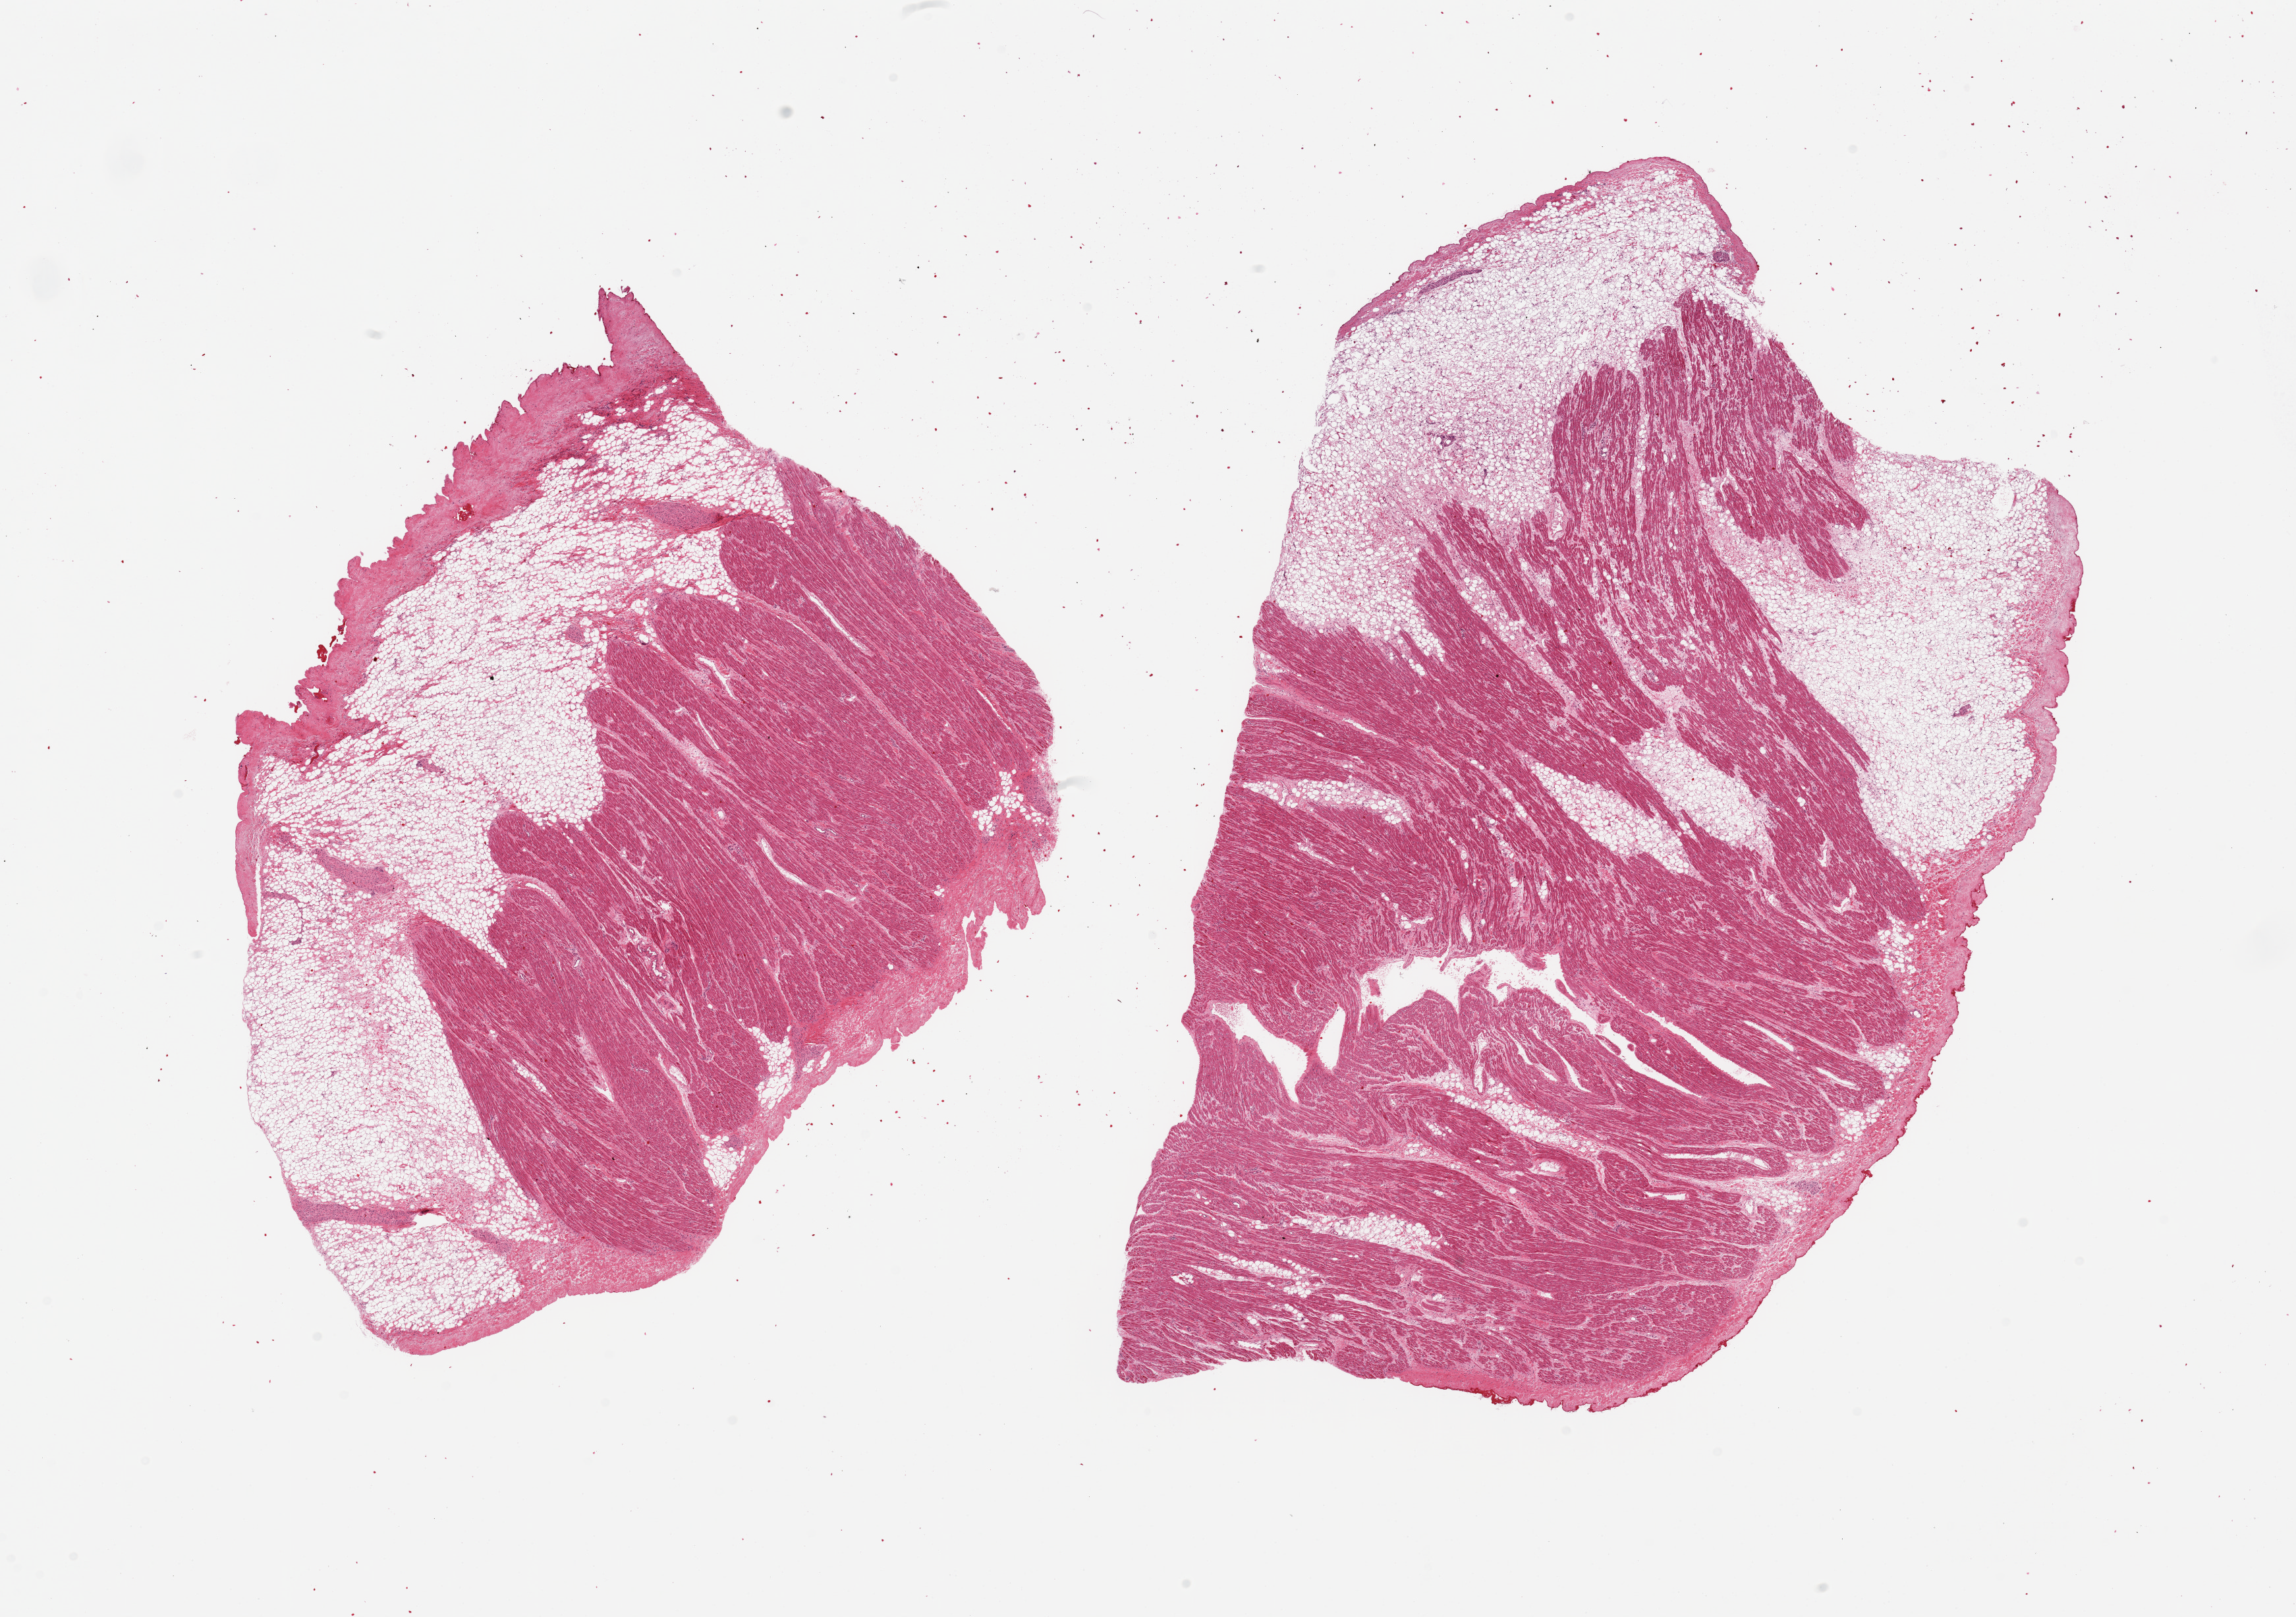
H&E whole-slide image — whole scanned area (about 27.6 x 19.4 mm) shown as a low-resolution overview; PAXgene-fixed, paraffin-embedded tissue; sampled site (target tissue): auricular appendage; tissue donor sample. Donor: male.
Reviewer comment on this tissue sample: 2 pieces; 30-40% is fat/nerve/ganglion cells.